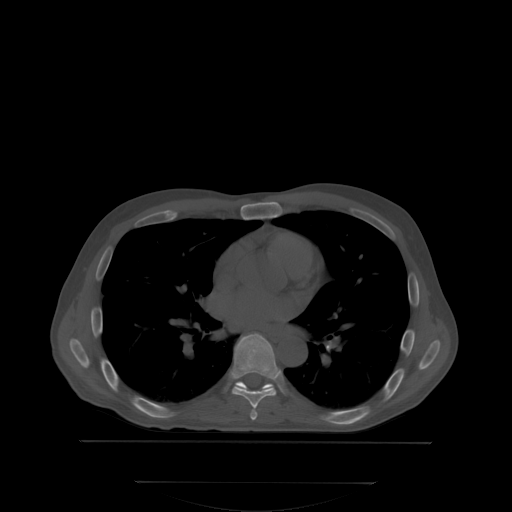
CT including the spine, one axial slice; slice 224 of 350 in the series (ordered by position); bone window (W 1800 / L 400 HU); 512 × 512 image matrix, field of view 500 × 500 mm. Patient: male, 58 years. Case-level facts recorded for this patient, not image findings: primary cancer: prostate; vertebrae with lytic lesions (as recorded): L1.
Outlined on this slice (semi-automatic segmentation, software-assisted and operator-edited):
- T6 vertebra: bounding box (x1, y1, x2, y2) in pixels: (251, 408, 257, 418)
- T7 vertebra: (232, 335, 277, 408)
- T8 vertebra: (235, 339, 272, 389)